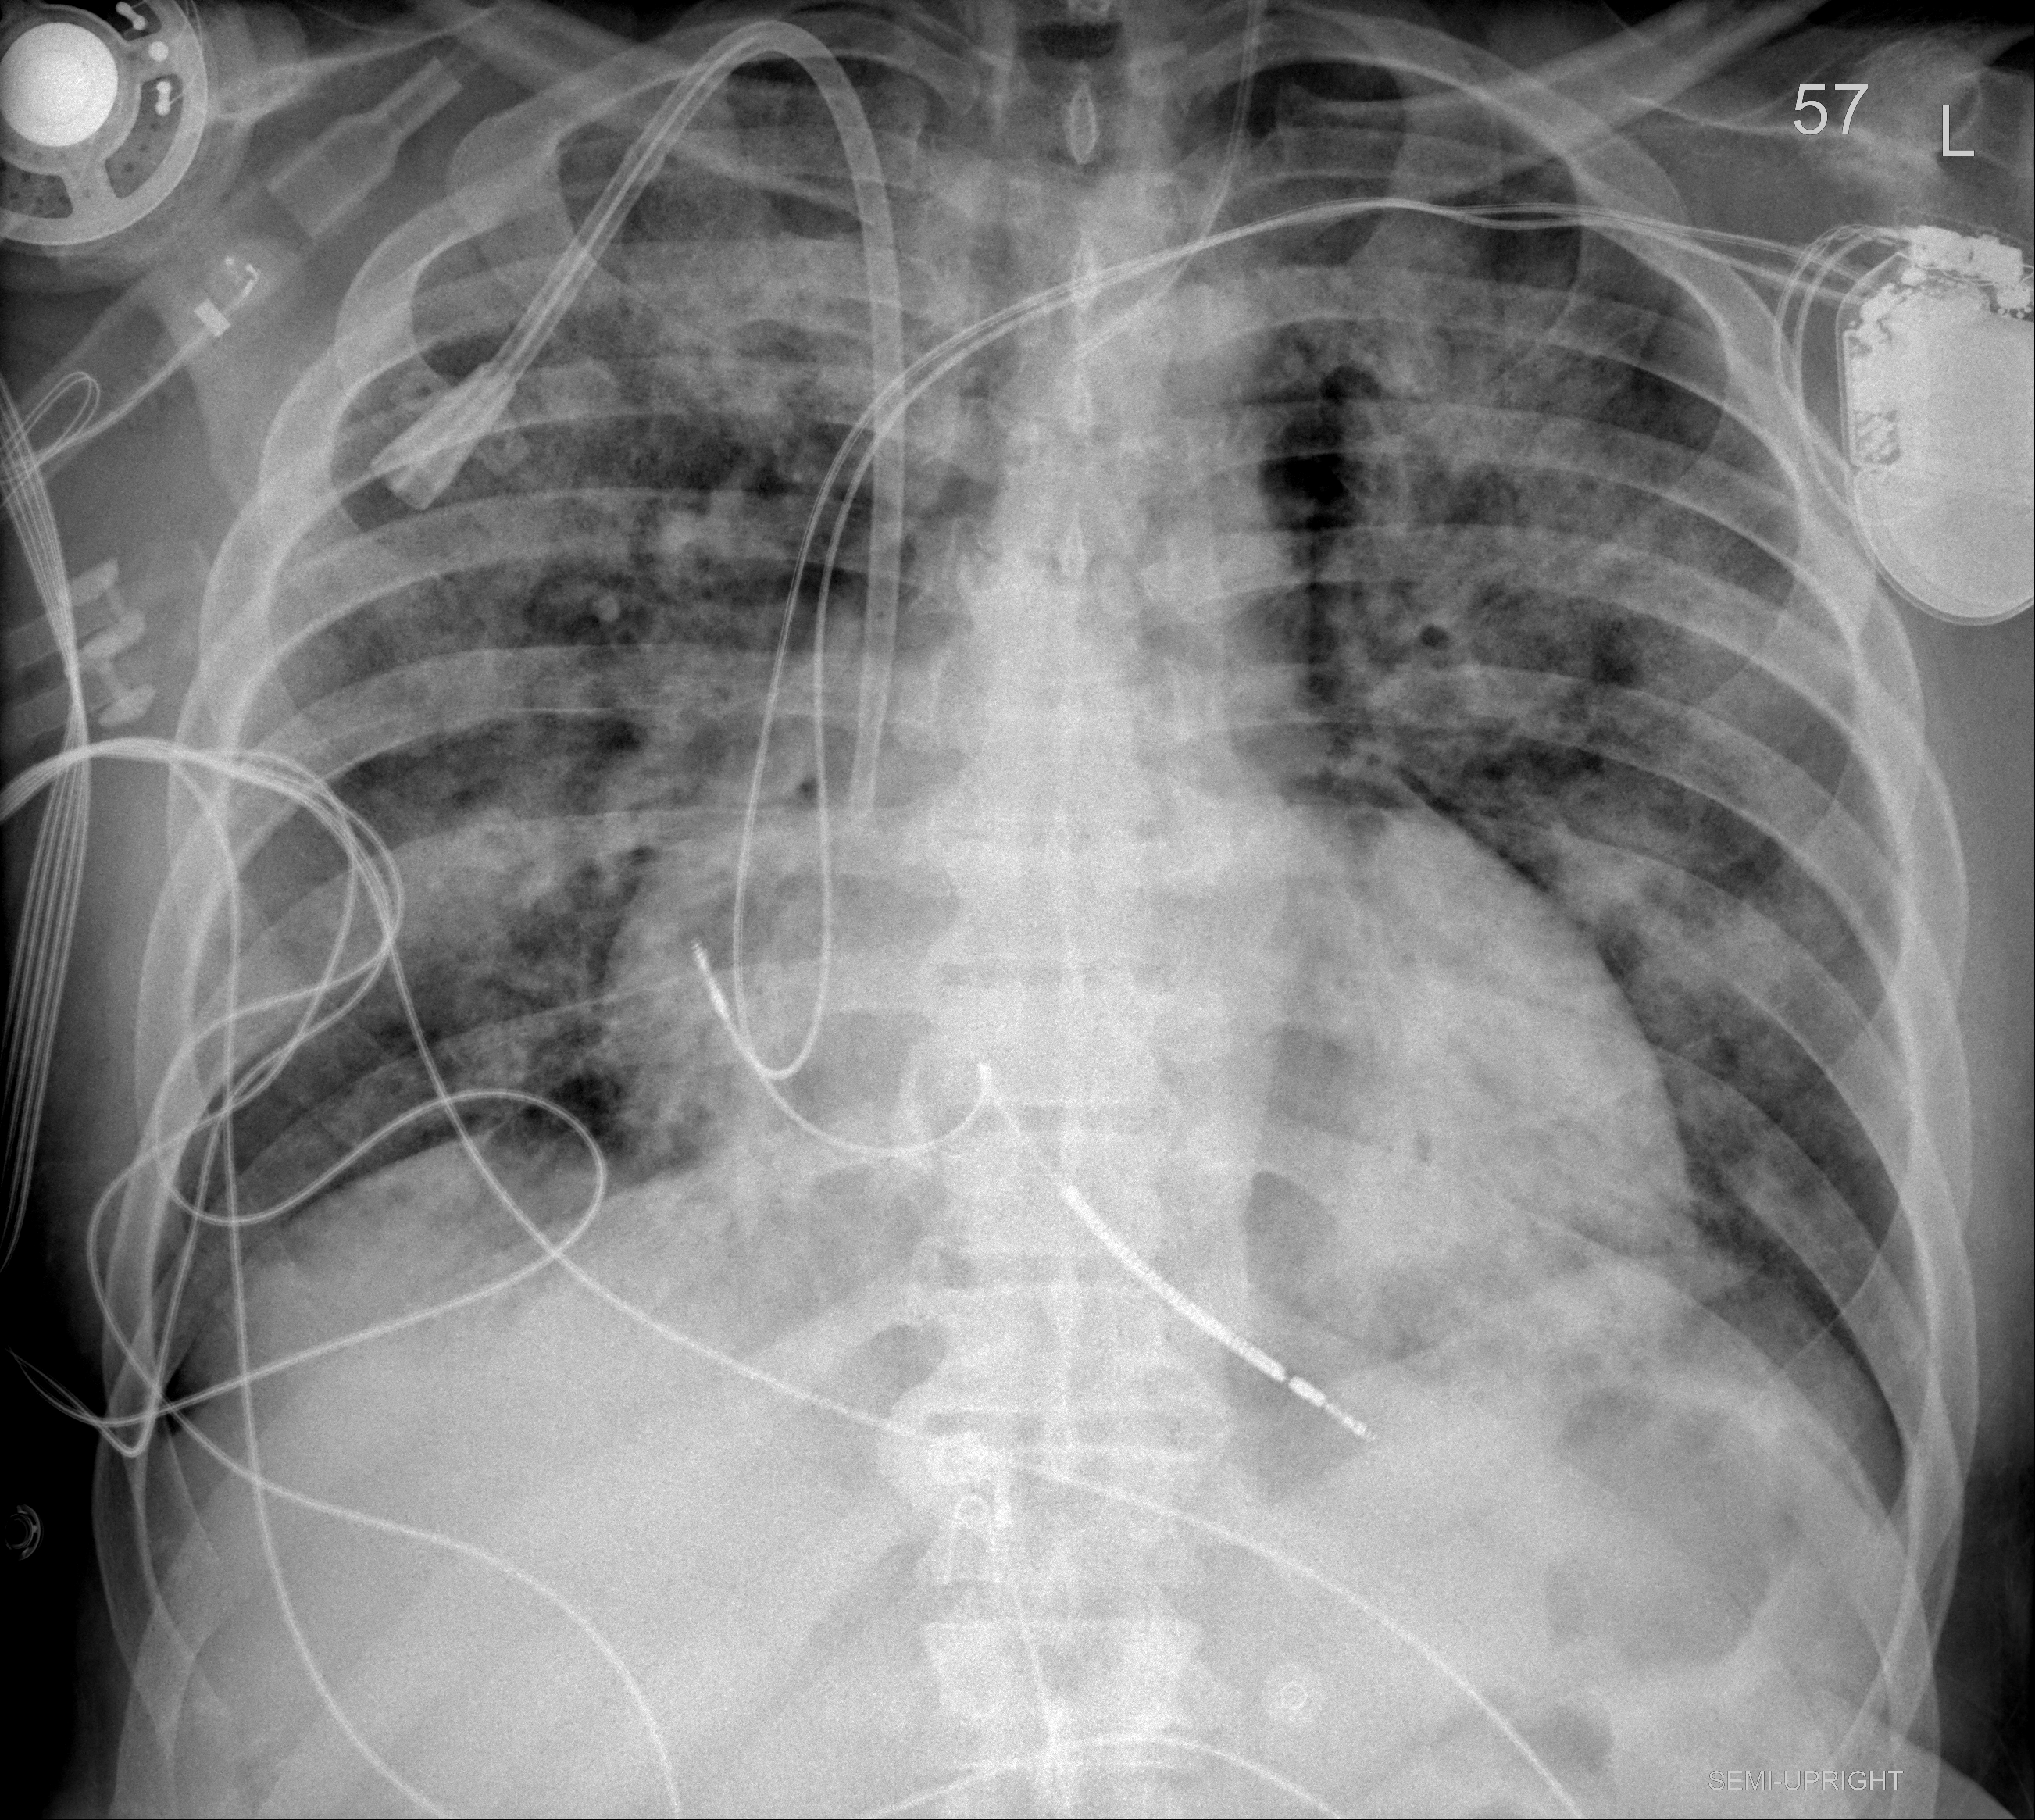
Chest X-ray (portable), AP projection. Male patient, age 60 years; imaged 7 days after the COVID-19 diagnosis.
Key findings recorded by the radiologist: Little change in the diffuse bilateral airspace disease.